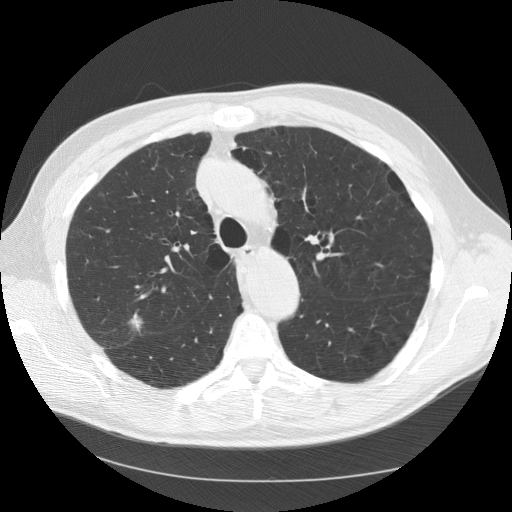
Low-dose screening chest CT, one axial slice; slice 92 of 133 in the series (ordered by position); reconstruction kernel STANDARD; lung window (W 1500 / L -600 HU); 512 × 512 image matrix, field of view 377 × 377 mm.
Annotated regions visible in this slice (outlined manually by an expert reader):
- lesion 1 (tumor, upper lobe of right lung): bounding box <129,313,143,332> (left, top, right, bottom; pixels)